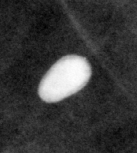
Region of interest cut from a scanned film mammogram (one marked finding); right breast; CC view; BI-RADS breast density category 1 (scale 1–4).
Marked abnormality: calcifications, morphology coarse; BI-RADS assessment category 2; subtlety rating 5 on a 1 (subtle) to 5 (obvious) scale; benign without callback (not worked up further).